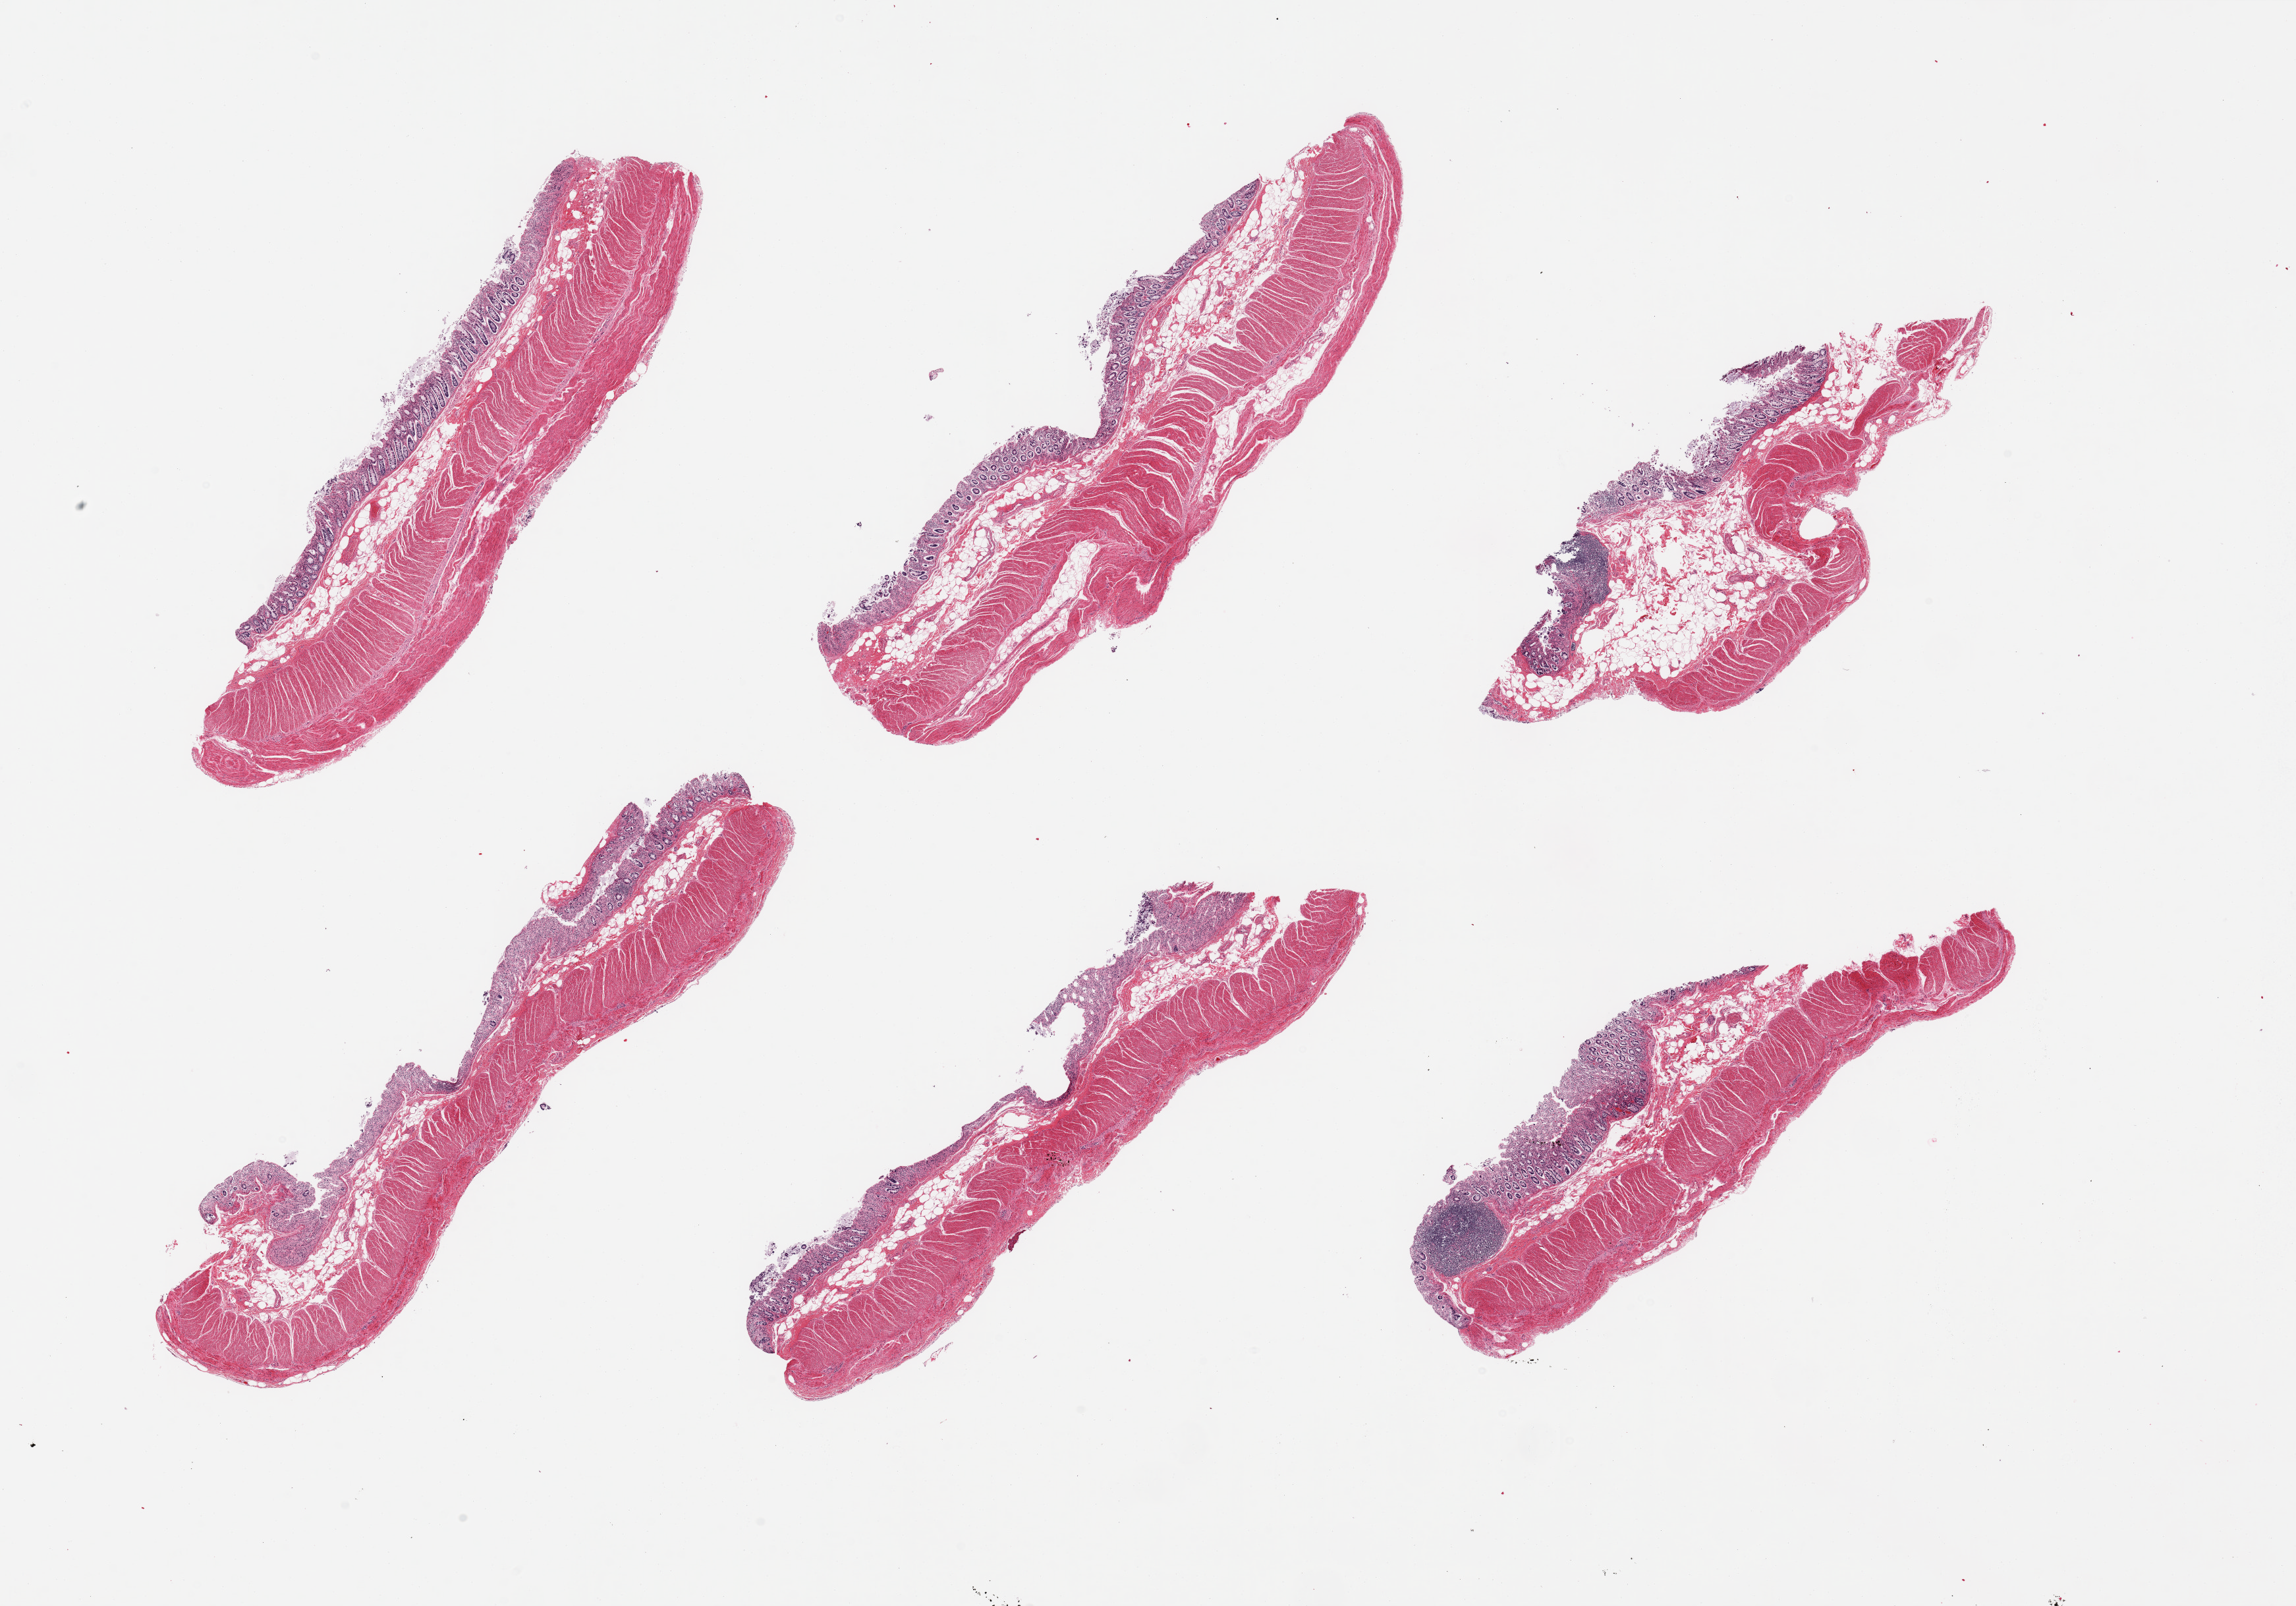
Digitized hematoxylin and eosin (H&E)-stained section, brightfield, whole scanned area (about 27.6 x 19.3 mm) shown as a low-resolution overview, PAXgene-fixed paraffin-embedded (PFPE) section, section of transverse colon (target tissue), donor tissue sample. Donor sex: male.
Review note (as recorded): 6 pieces, mucosa up to ~0.4mm, ~20% thickness.